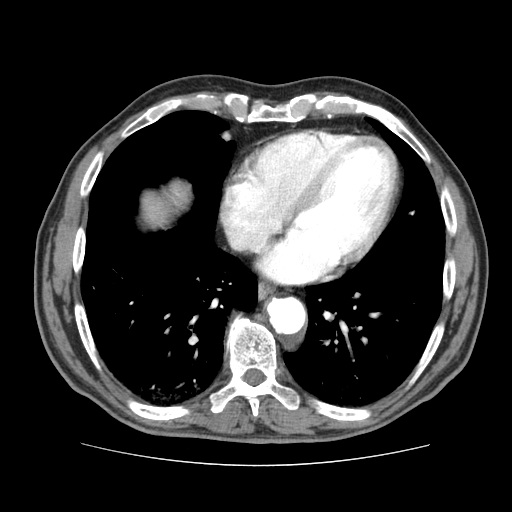
Contrast-enhanced abdominal CT (liver protocol), one axial slice. Slice 76 of 79 in the series (ordered by position). Soft-tissue window (W 400 / L 40 HU). 512 × 512 image matrix, field of view 360 × 360 mm. Case-level facts recorded for this patient, not image findings: diagnosis: hepatocellular carcinoma (patient treated with transarterial chemoembolisation; whether this scan precedes or follows treatment is not stated here); TNM stage (as recorded): Stage-I; Child-Pugh class: A.
Annotated regions visible in this slice (semi-automatic segmentation, software-assisted and operator-edited):
- abdominal aorta: bounding box <267,297,305,333> (left, top, right, bottom; pixels)
- liver parenchyma outside the tumour (the mass and vessels are separate outlines, so this box may not span the whole liver): <144,184,188,220>